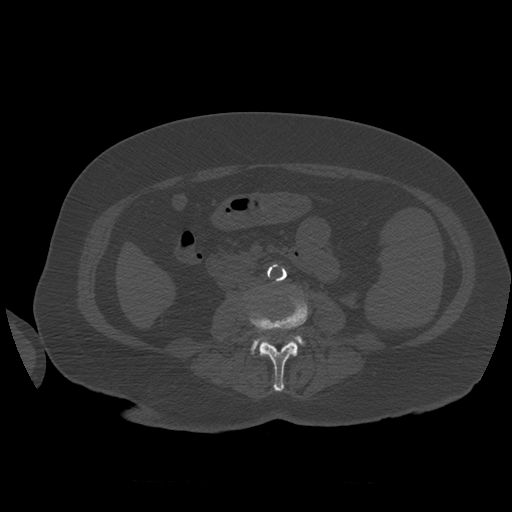
CT including the spine, one axial slice; slice 222 of 399 in the series (ordered by position); bone window (W 1800 / L 400 HU); 512 × 512 image matrix, field of view 404 × 404 mm. Patient age 81 years. Case-level facts recorded for this patient, not image findings: primary cancer: renal; vertebrae with lytic lesions (as recorded): L1.
Outlined on this slice (semi-automatically segmented with operator editing):
- L3 vertebra: bounding box (x1, y1, x2, y2) in pixels: (250, 291, 308, 392)
- L4 vertebra: (251, 336, 305, 355)